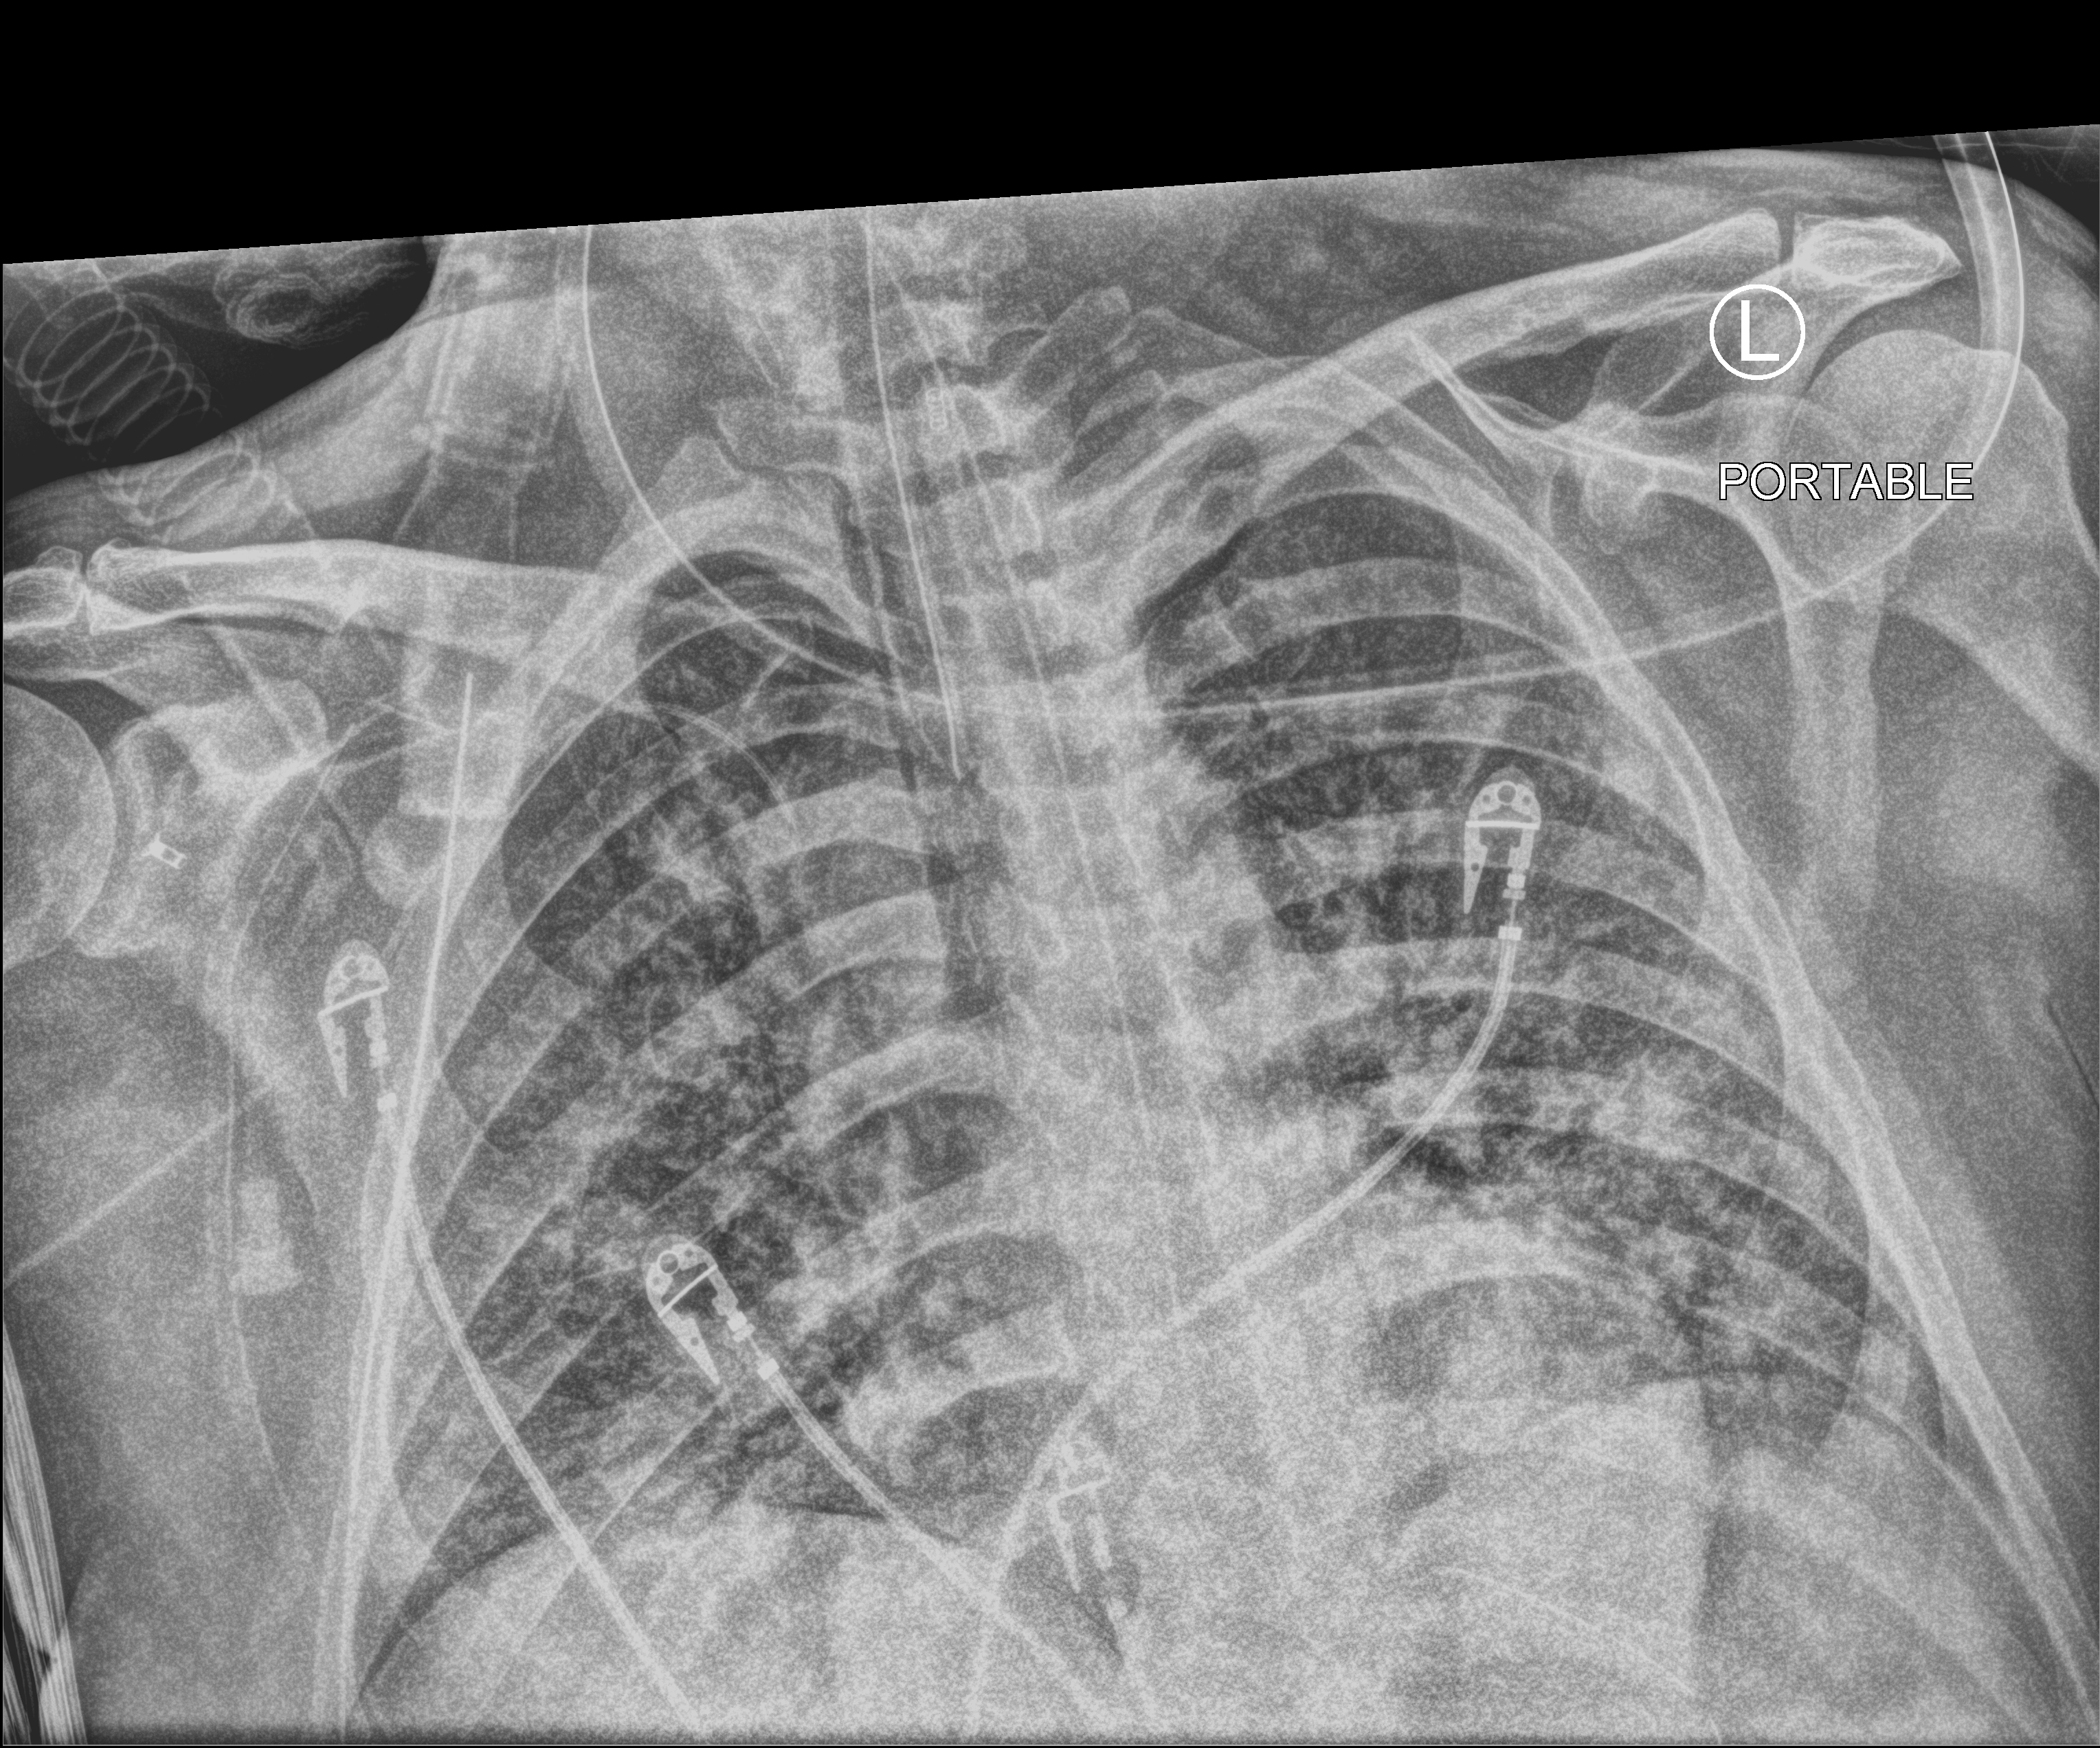
Chest X-ray (portable); anteroposterior (AP) projection. Male patient hospitalised with COVID-19, age 18–59 years.
Admission-level facts for this patient (not findings on this image; timing relative to this image not recorded): chronic kidney disease (admission record): no; mechanically ventilated during this hospital stay: yes.